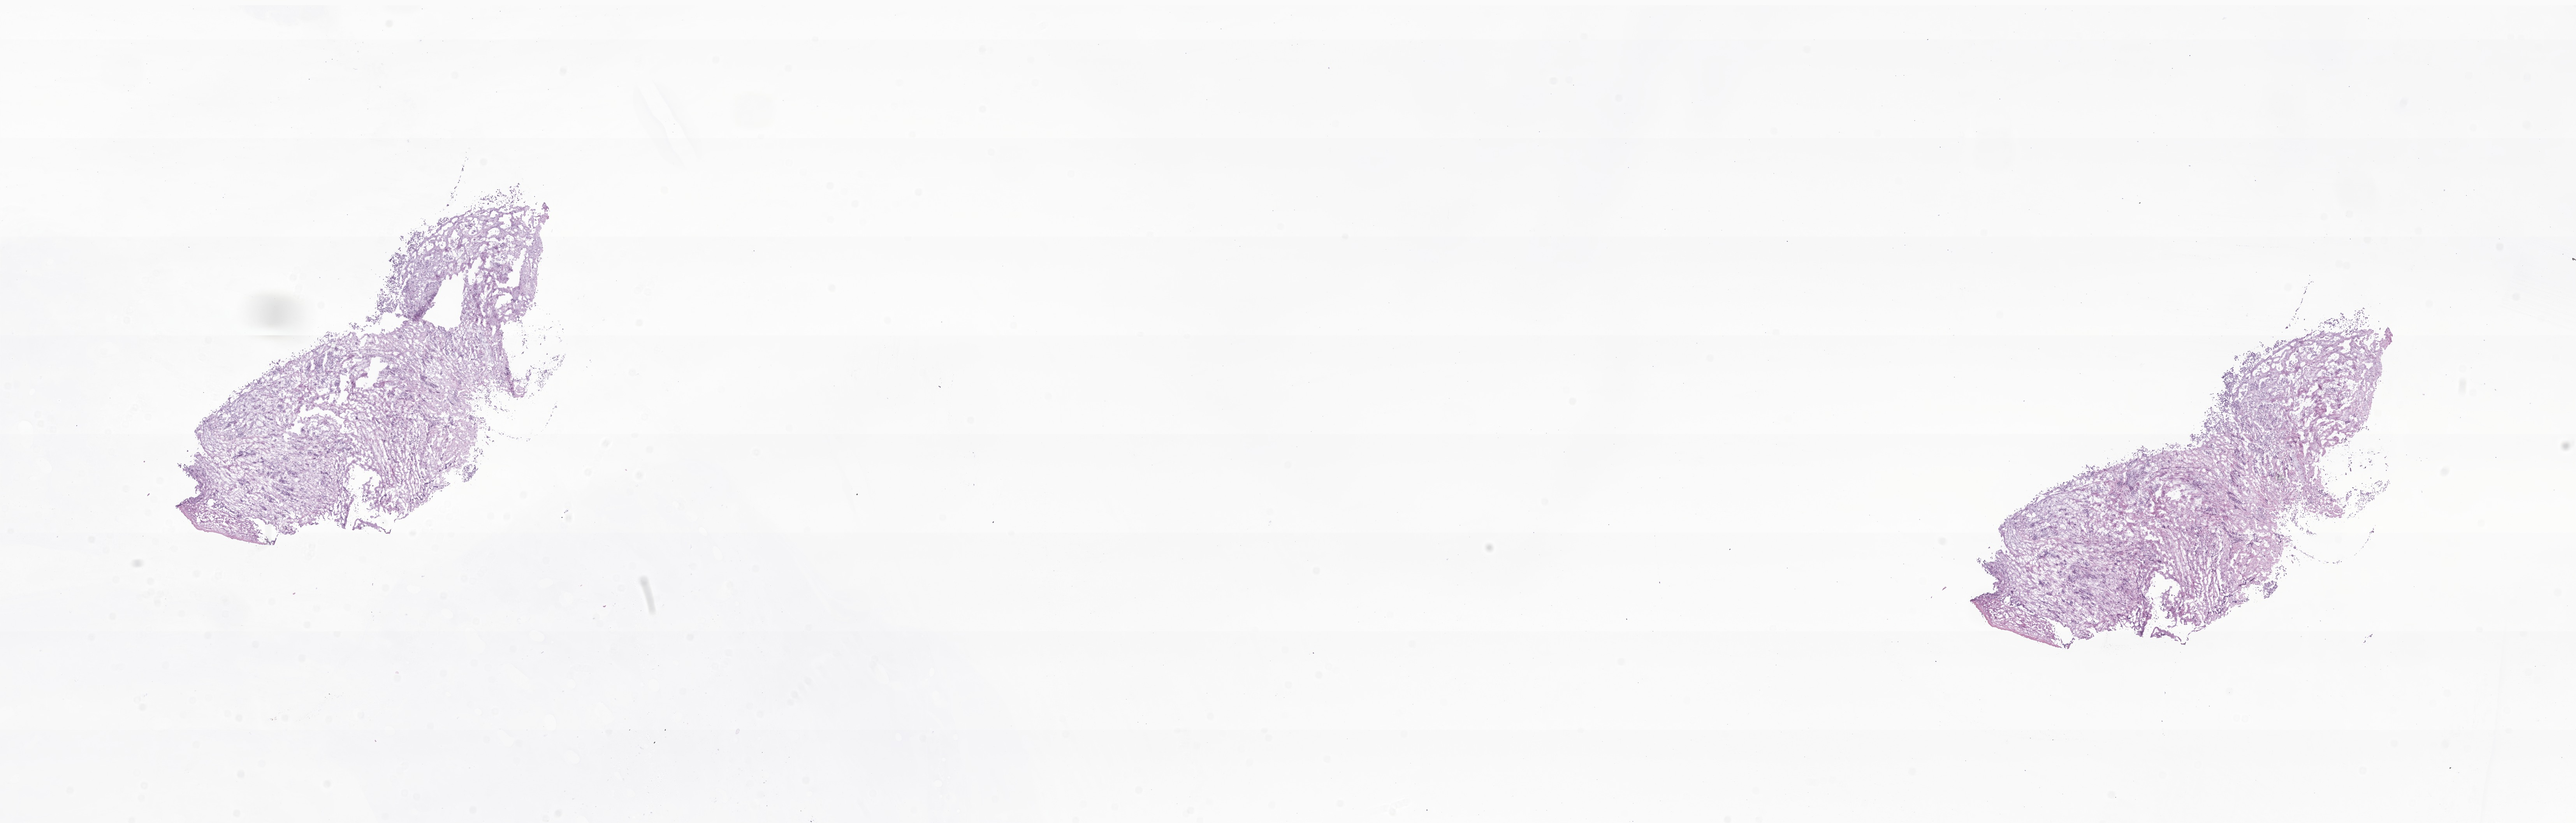
Digitized H&E-stained section of tumor tissue from the abdomen, a low-resolution overview of the entire scanned area, about 27.9 x 8.9 mm, cryosection (OCT / tissue freezing medium). Patient female; age 118 months (9 years 10 months).
Recorded diagnosis: Desmoplastic small round cell tumor.